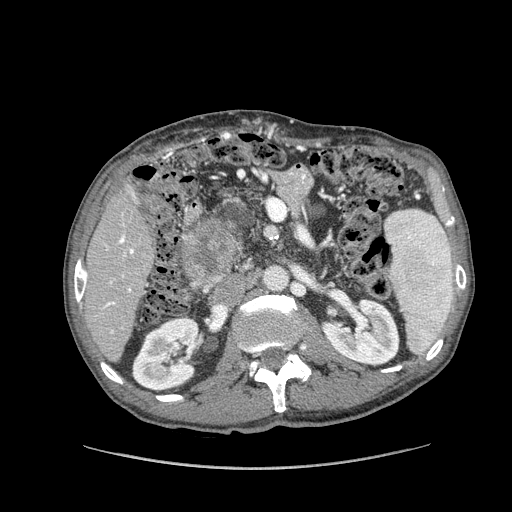
Contrast-enhanced abdominal CT (liver protocol), one axial slice; position 45 of 162 along the scan axis; reconstruction kernel STANDARD; 100 kVp; soft-tissue window (W 400 / L 40 HU); 2.5 mm slice thickness; 512 × 512 image matrix, field of view 400 × 400 mm. Case-level facts recorded for this patient, not image findings: diagnosis: hepatocellular carcinoma (patient treated with transarterial chemoembolisation; whether this scan precedes or follows treatment is not stated here); TNM stage (as recorded): Stage-IIIA.
Outlined on this slice (semi-automatically segmented with operator editing):
- liver parenchyma outside the tumour (the mass and vessels are separate outlines, so this box may not span the whole liver): bounding box [x1, y1, x2, y2] px = [82, 180, 154, 360]
- mass: [184, 218, 237, 285]
- liver vessels: [83, 193, 135, 334]